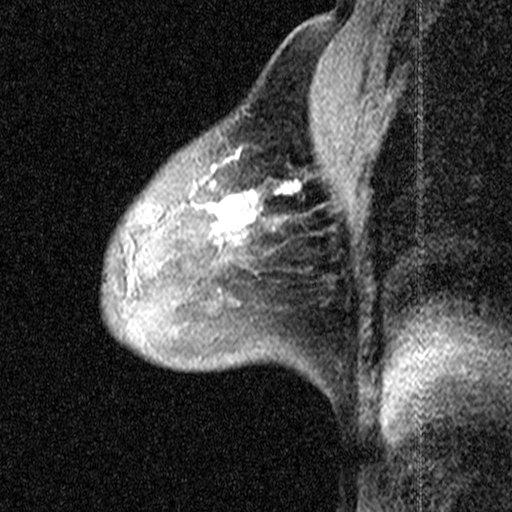
Breast MRI (dynamic contrast-enhanced), one sagittal slice; slice 30 of 44 in the series (ordered by position); dynamic contrast-enhanced study with each time point stored as its own series, time point 2 of 3 at this slice position (early post-contrast, ordered by acquisition time); 1.5 T; TE 4.5 ms, TR 11 ms; 3 mm slice thickness; 512 × 512 image matrix, field of view 200 × 200 mm. Female patient, age 53 years. From the clinical record (not read from this slice): setting: breast cancer imaged before/during neoadjuvant chemotherapy; receptor status: HR-positive, HER2-negative.
Outlined on this slice (semi-automatic segmentation, software-assisted and operator-edited):
- analysis volume of interest (the breast-tissue region the enhancement analysis was run in; not a lesion): bounding box [x1, y1, x2, y2] px = [198, 152, 299, 267]
- tumour enhancement mask (voxels above the 90 % enhancement threshold inside the analysis volume of interest): [211, 181, 299, 230]